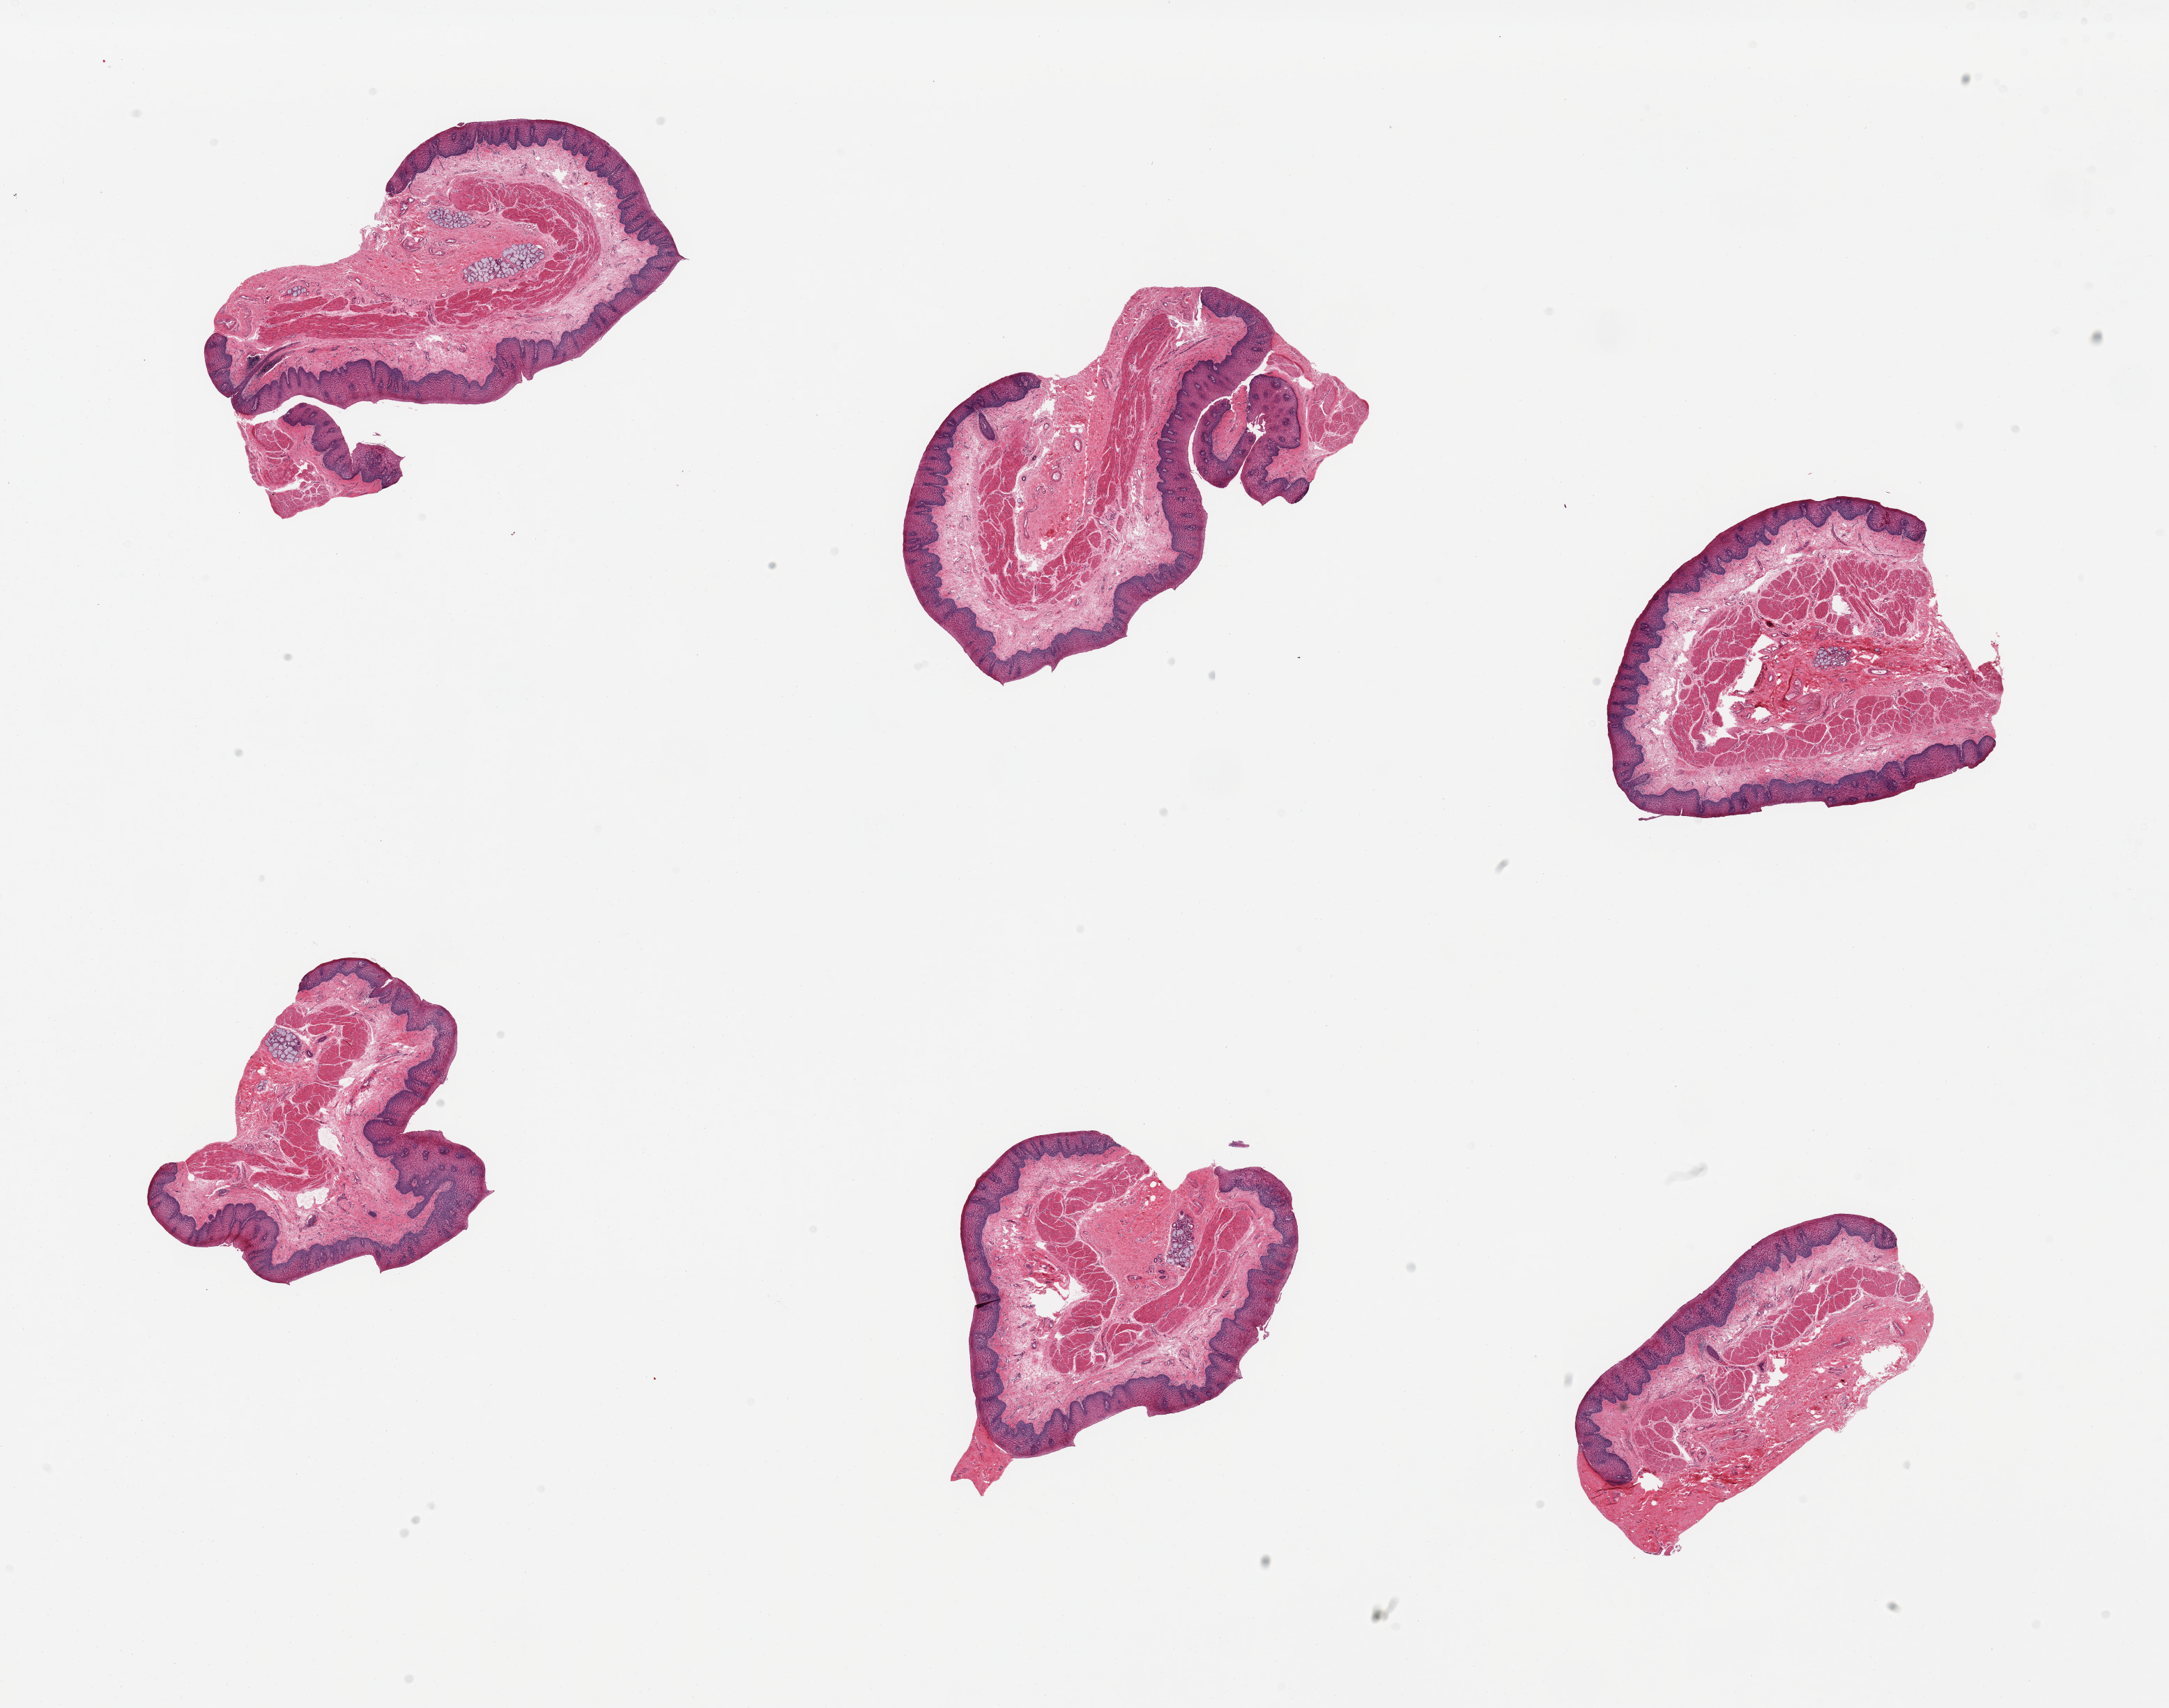
Hematoxylin and eosin (H&E) whole-slide image, brightfield, a low-resolution overview of the entire scanned area, about 24.6 x 19.4 mm. PAXgene-fixed, paraffin-embedded tissue. Sampled site (target tissue): esophageal mucous membrane. Tissue donor sample. Donor: male.
Reviewer comment on this tissue sample: 6 pieces; includes several clusters of submucosal glands.